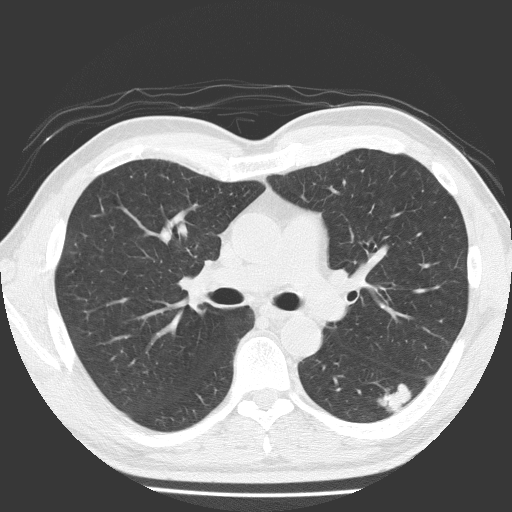
Low-dose screening chest CT, one axial slice; position 111 of 184 along the scan axis; lung window (W 1500 / L -600 HU); 512 × 512 image matrix, field of view 348 × 348 mm.
Structures marked on this image (manually delineated by an expert):
- lesion 1 (tumor, lower lobe of left lung): box from (x=378, y=383) to (x=412, y=415) px